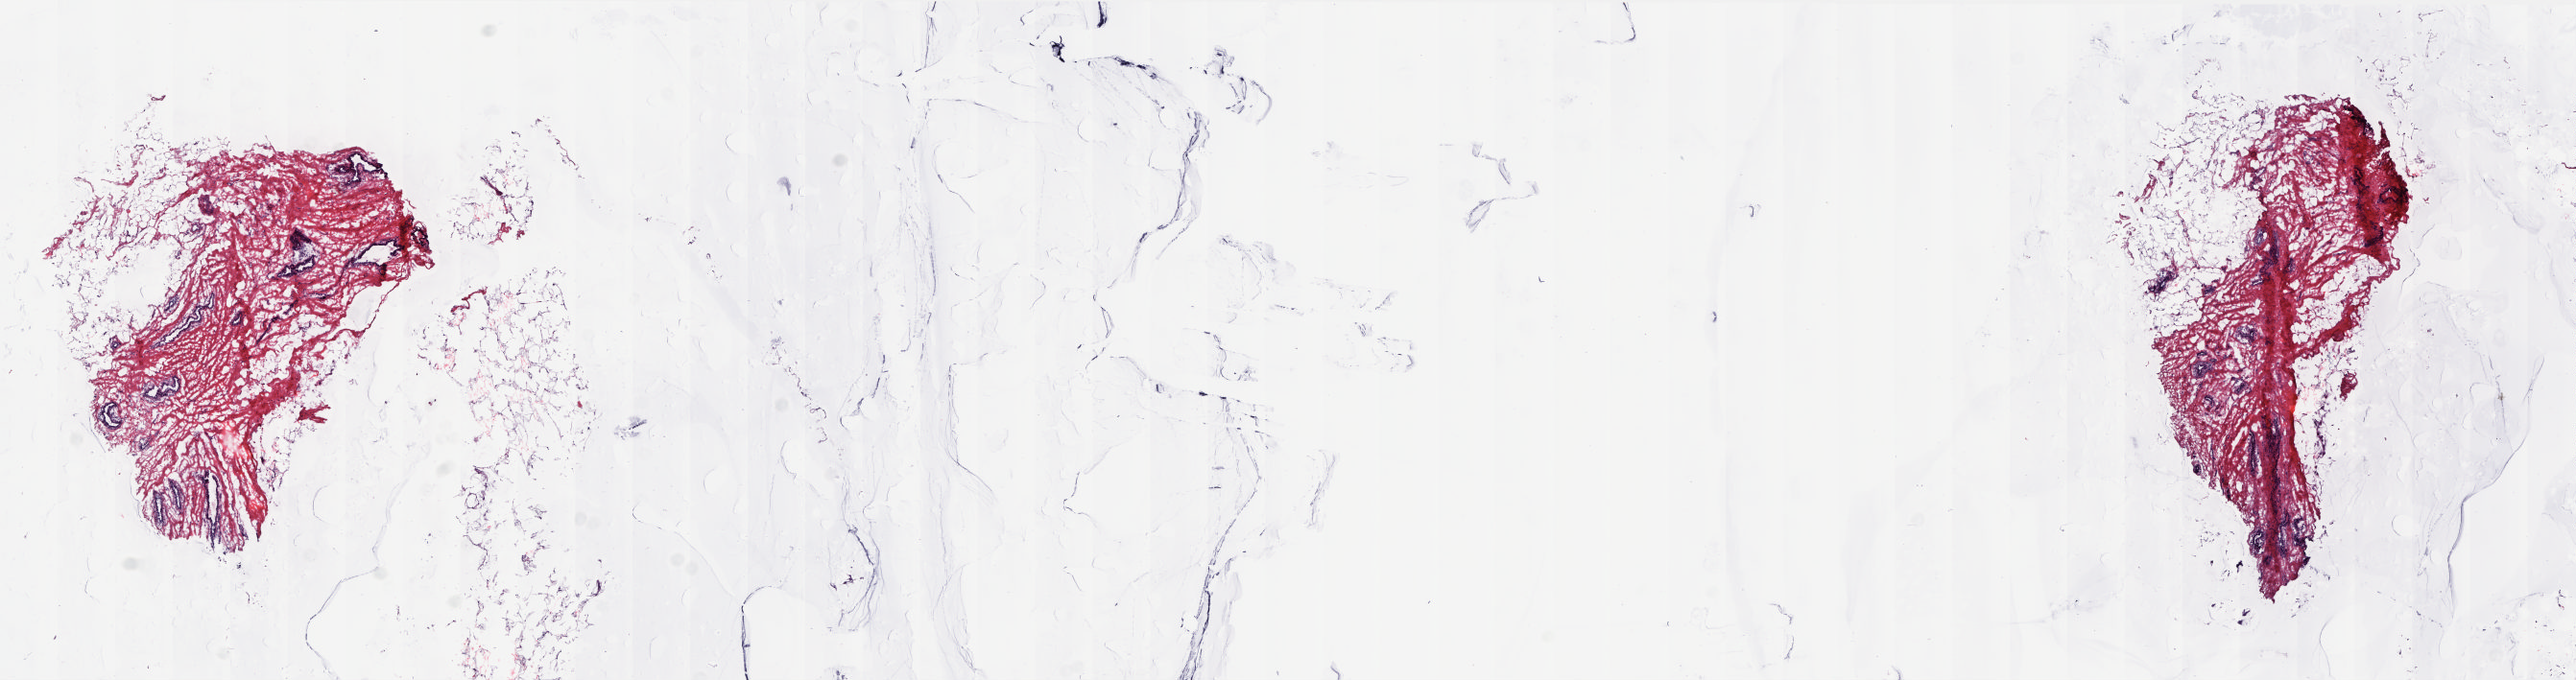
H&E whole-slide image, low-resolution overview of the scanned area, about 21.6 x 5.7 mm; frozen section; breast, solid tissue normal (non-tumour tissue) sample. Female patient; age at initial diagnosis 62 years. Composition of this section per pathologist review: tumour cells 0%, tumour nuclei 0%, normal cells 12%, stromal cells 88%, necrosis 0%. Infiltration values recorded for this section: lymphocyte infiltration 1%, monocyte infiltration 0%, neutrophil infiltration 0%.
This section: solid tissue normal (non-tumour) sample from the same patient. Patient diagnosis: Lobular carcinoma, NOS.